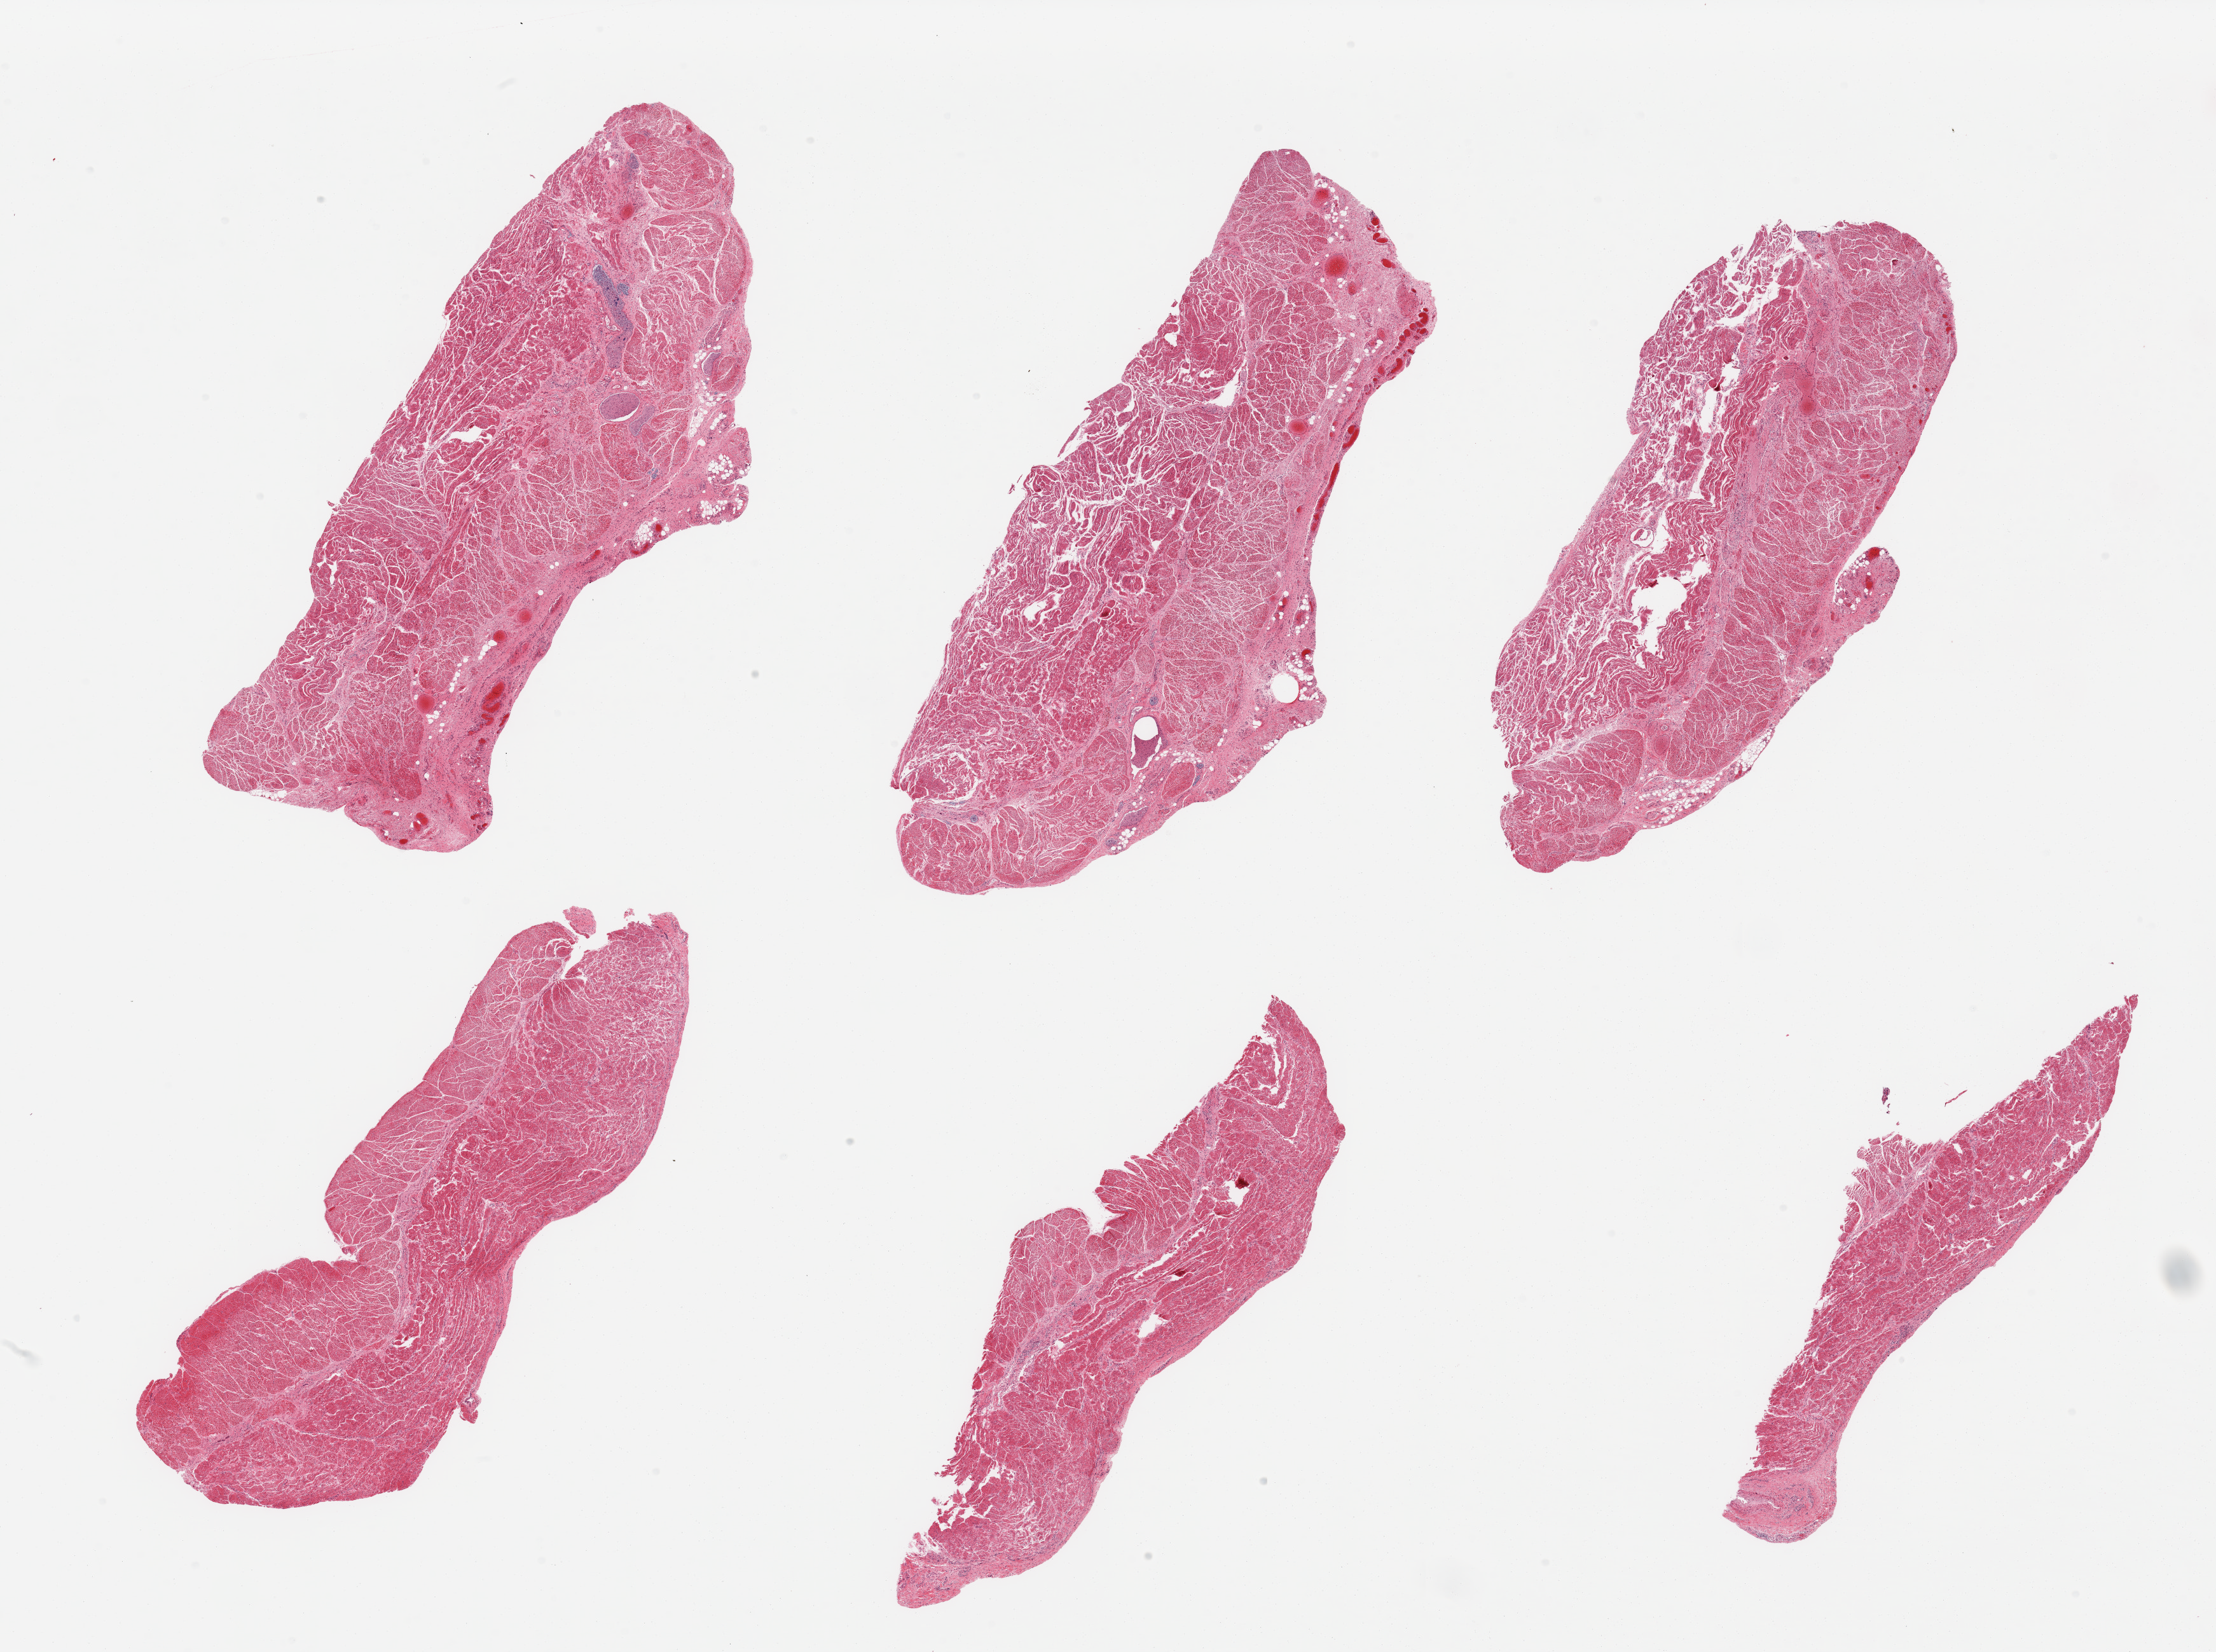
Digitized haematoxylin and eosin-stained section, whole scanned area (about 27.6 x 20.5 mm, acquisition: 20x scan) shown as a low-resolution overview. PAXgene-fixed paraffin-embedded (PFPE) section. Sampled site (target tissue): gastroesophageal junction. Tissue donor sample. Donor: male.
Reviewer comment on this tissue sample: 6 pieces; target muscularis.